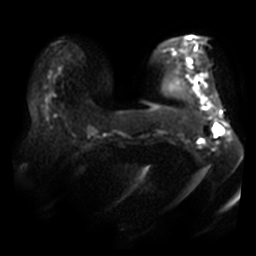
Breast MRI, one axial slice. Position 9 of 40 along the scan axis. Diffusion-weighted series; image 2 of 4 stored at this slice position (different b-values; order by instance number). 3 T. 5 mm slice thickness. 256 × 256 image matrix, field of view 400 × 400 mm. Female patient.
Structures marked on this image (outlined manually by an expert reader):
- tumour on diffusion-weighted imaging: bounding box (x1, y1, x2, y2) in pixels: (216, 125, 225, 134)